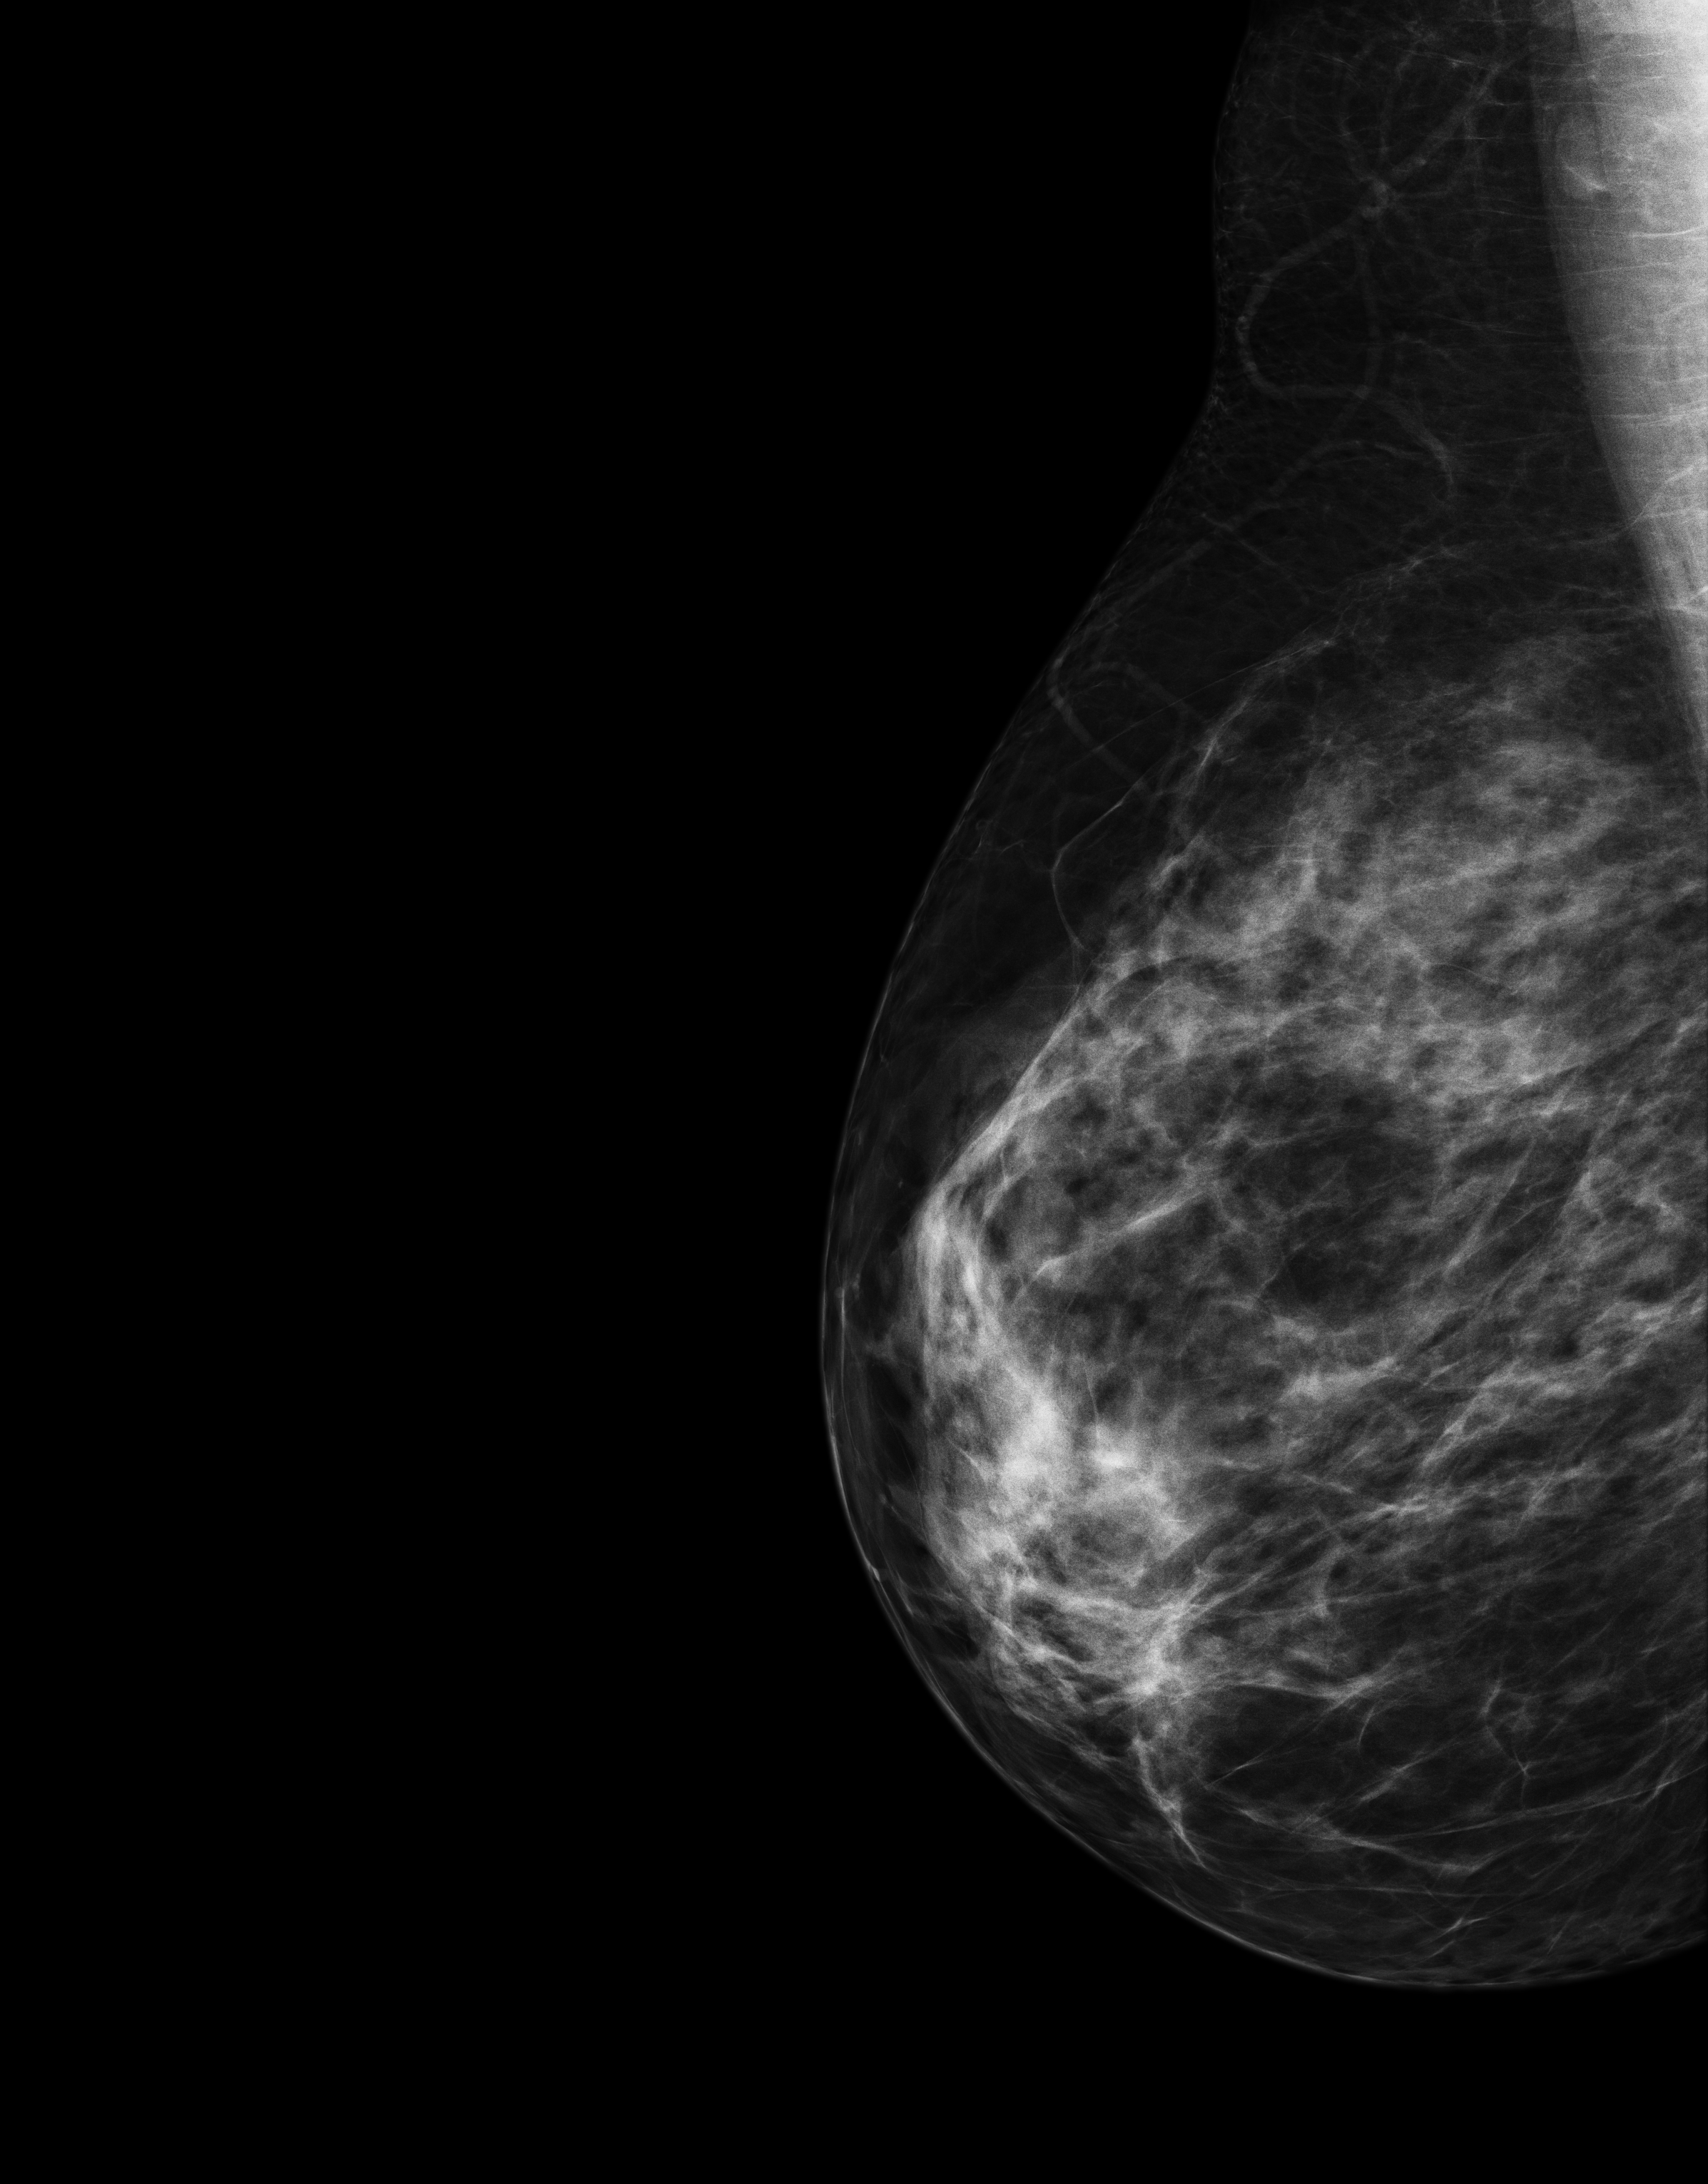
Digital mammogram (FFDM); right breast; laterally exaggerated craniocaudal (XCCL) view; annual screening mammography examination; compressed breast thickness 83 mm. Patient: female, 42 years.
BI-RADS breast density category at the screening exam (both breasts, scale 1–4): 3. Final BI-RADS assessment for this screening round (tomosynthesis exam, both breasts): category 1. Recall: no recall after this screen.